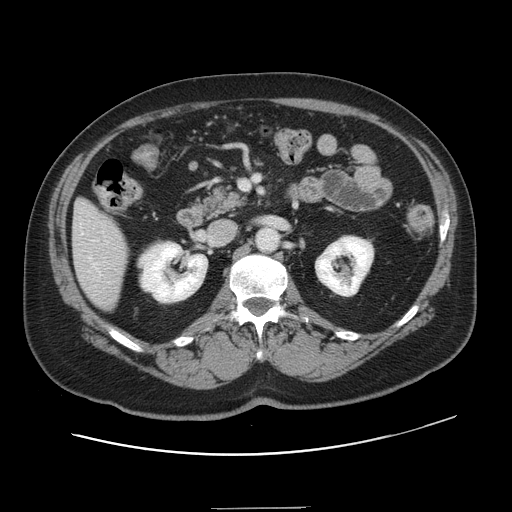
Contrast-enhanced abdominal CT, one axial slice; 120 kVp; intravenous contrast given; soft-tissue window (W 400 / L 40 HU); 512 × 512 image matrix, field of view 402 × 402 mm. Male patient, age 62 years. From the clinical record (not read from this slice): diagnosis: colorectal cancer liver metastases, imaged before liver resection; multiple liver metastases: yes; largest metastasis: 2.7 cm; disease in both lobes: no.
Annotated regions visible in this slice (manually delineated by an expert):
- hepatic veins: box from (x=81, y=233) to (x=97, y=268) px
- liver: (x=73, y=201)–(x=129, y=310)
- portal vein (with intrahepatic branches): (x=95, y=240)–(x=108, y=243)